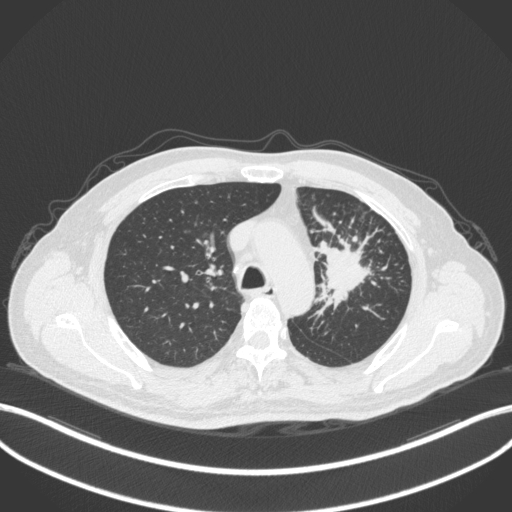
Chest CT, one axial slice. Slice 257 of 386 in the series (ordered by position). 120 kVp. Lung window (W 1500 / L -600 HU). 512 × 512 image matrix. Patient: male, 69 years. From the clinical record (not read from this slice): clinical TNM (as recorded): T2a N2 M0; histopathological grade: G2-3.
Outlined on this slice (rectangle marked by the reading radiologist):
- lung tumour (recorded histology: adenocarcinoma): bounding box <317,238,374,311> (left, top, right, bottom; pixels)